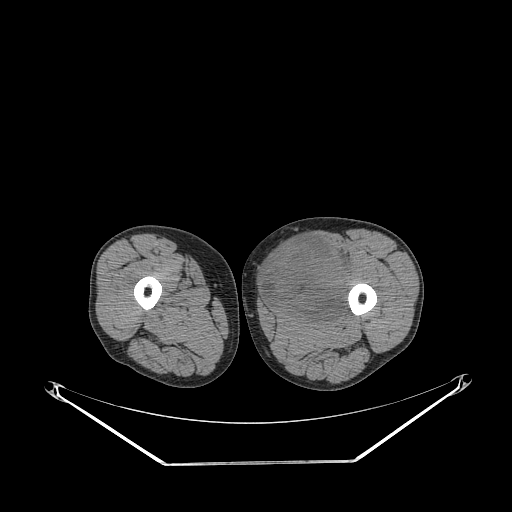
CT of an extremity soft-tissue mass (from a PET/CT study), one axial slice. Reconstruction kernel STANDARD. 140 kVp. Soft-tissue window (W 400 / L 40 HU). 3.75 mm slice thickness. 512 × 512 image matrix, field of view 500 × 500 mm. Male patient. From the clinical record (not read from this slice): histological type: pleiomorphic liposarcoma; grade: high; site of the primary tumour: left thigh.
Structures marked on this image (expert contour drawn on MRI and transferred to this co-registered scan by the dataset authors):
- gross tumour volume including surrounding oedema: bounding box (x1, y1, x2, y2) in pixels: (263, 237, 355, 321)
- gross tumour volume (mass): (263, 237, 350, 321)